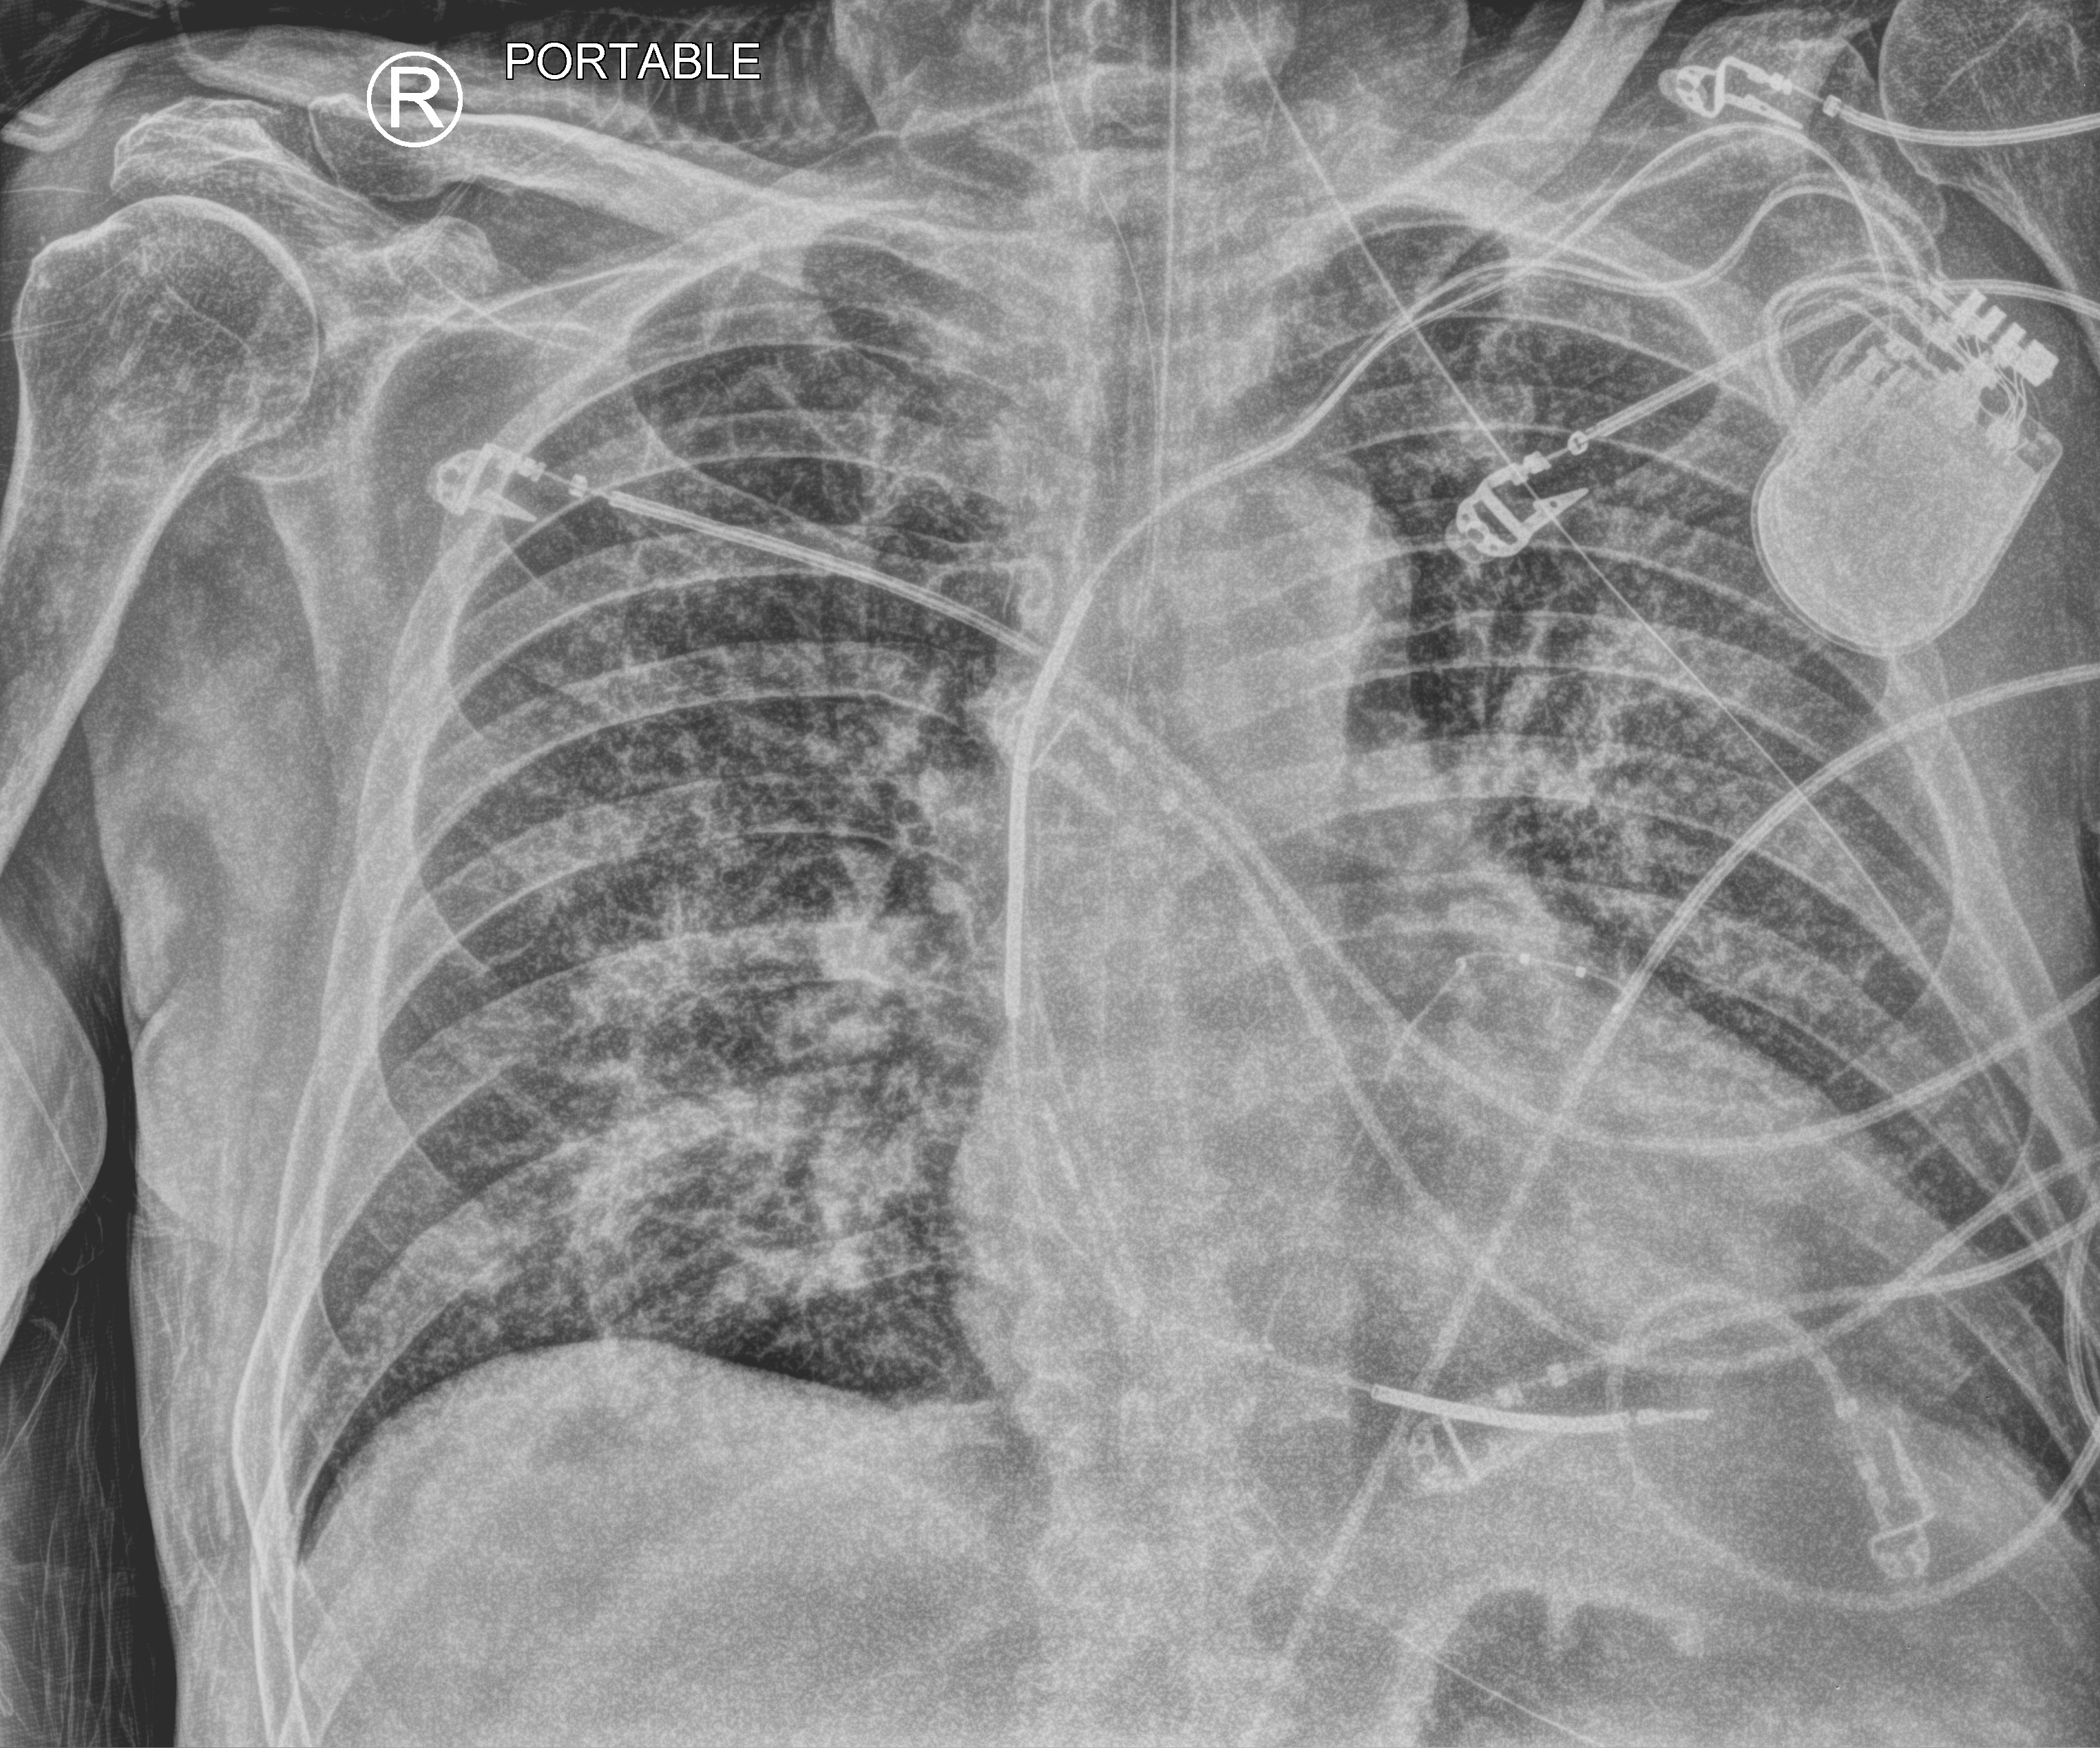
Chest X-ray (portable); anteroposterior (AP) projection. Patient hospitalised with COVID-19; male, aged 60–74 years.
Hospital-stay facts (about this admission, not read from this image; timing relative to this image not recorded): hypertension (admission record): yes; mechanically ventilated during this hospital stay: yes.